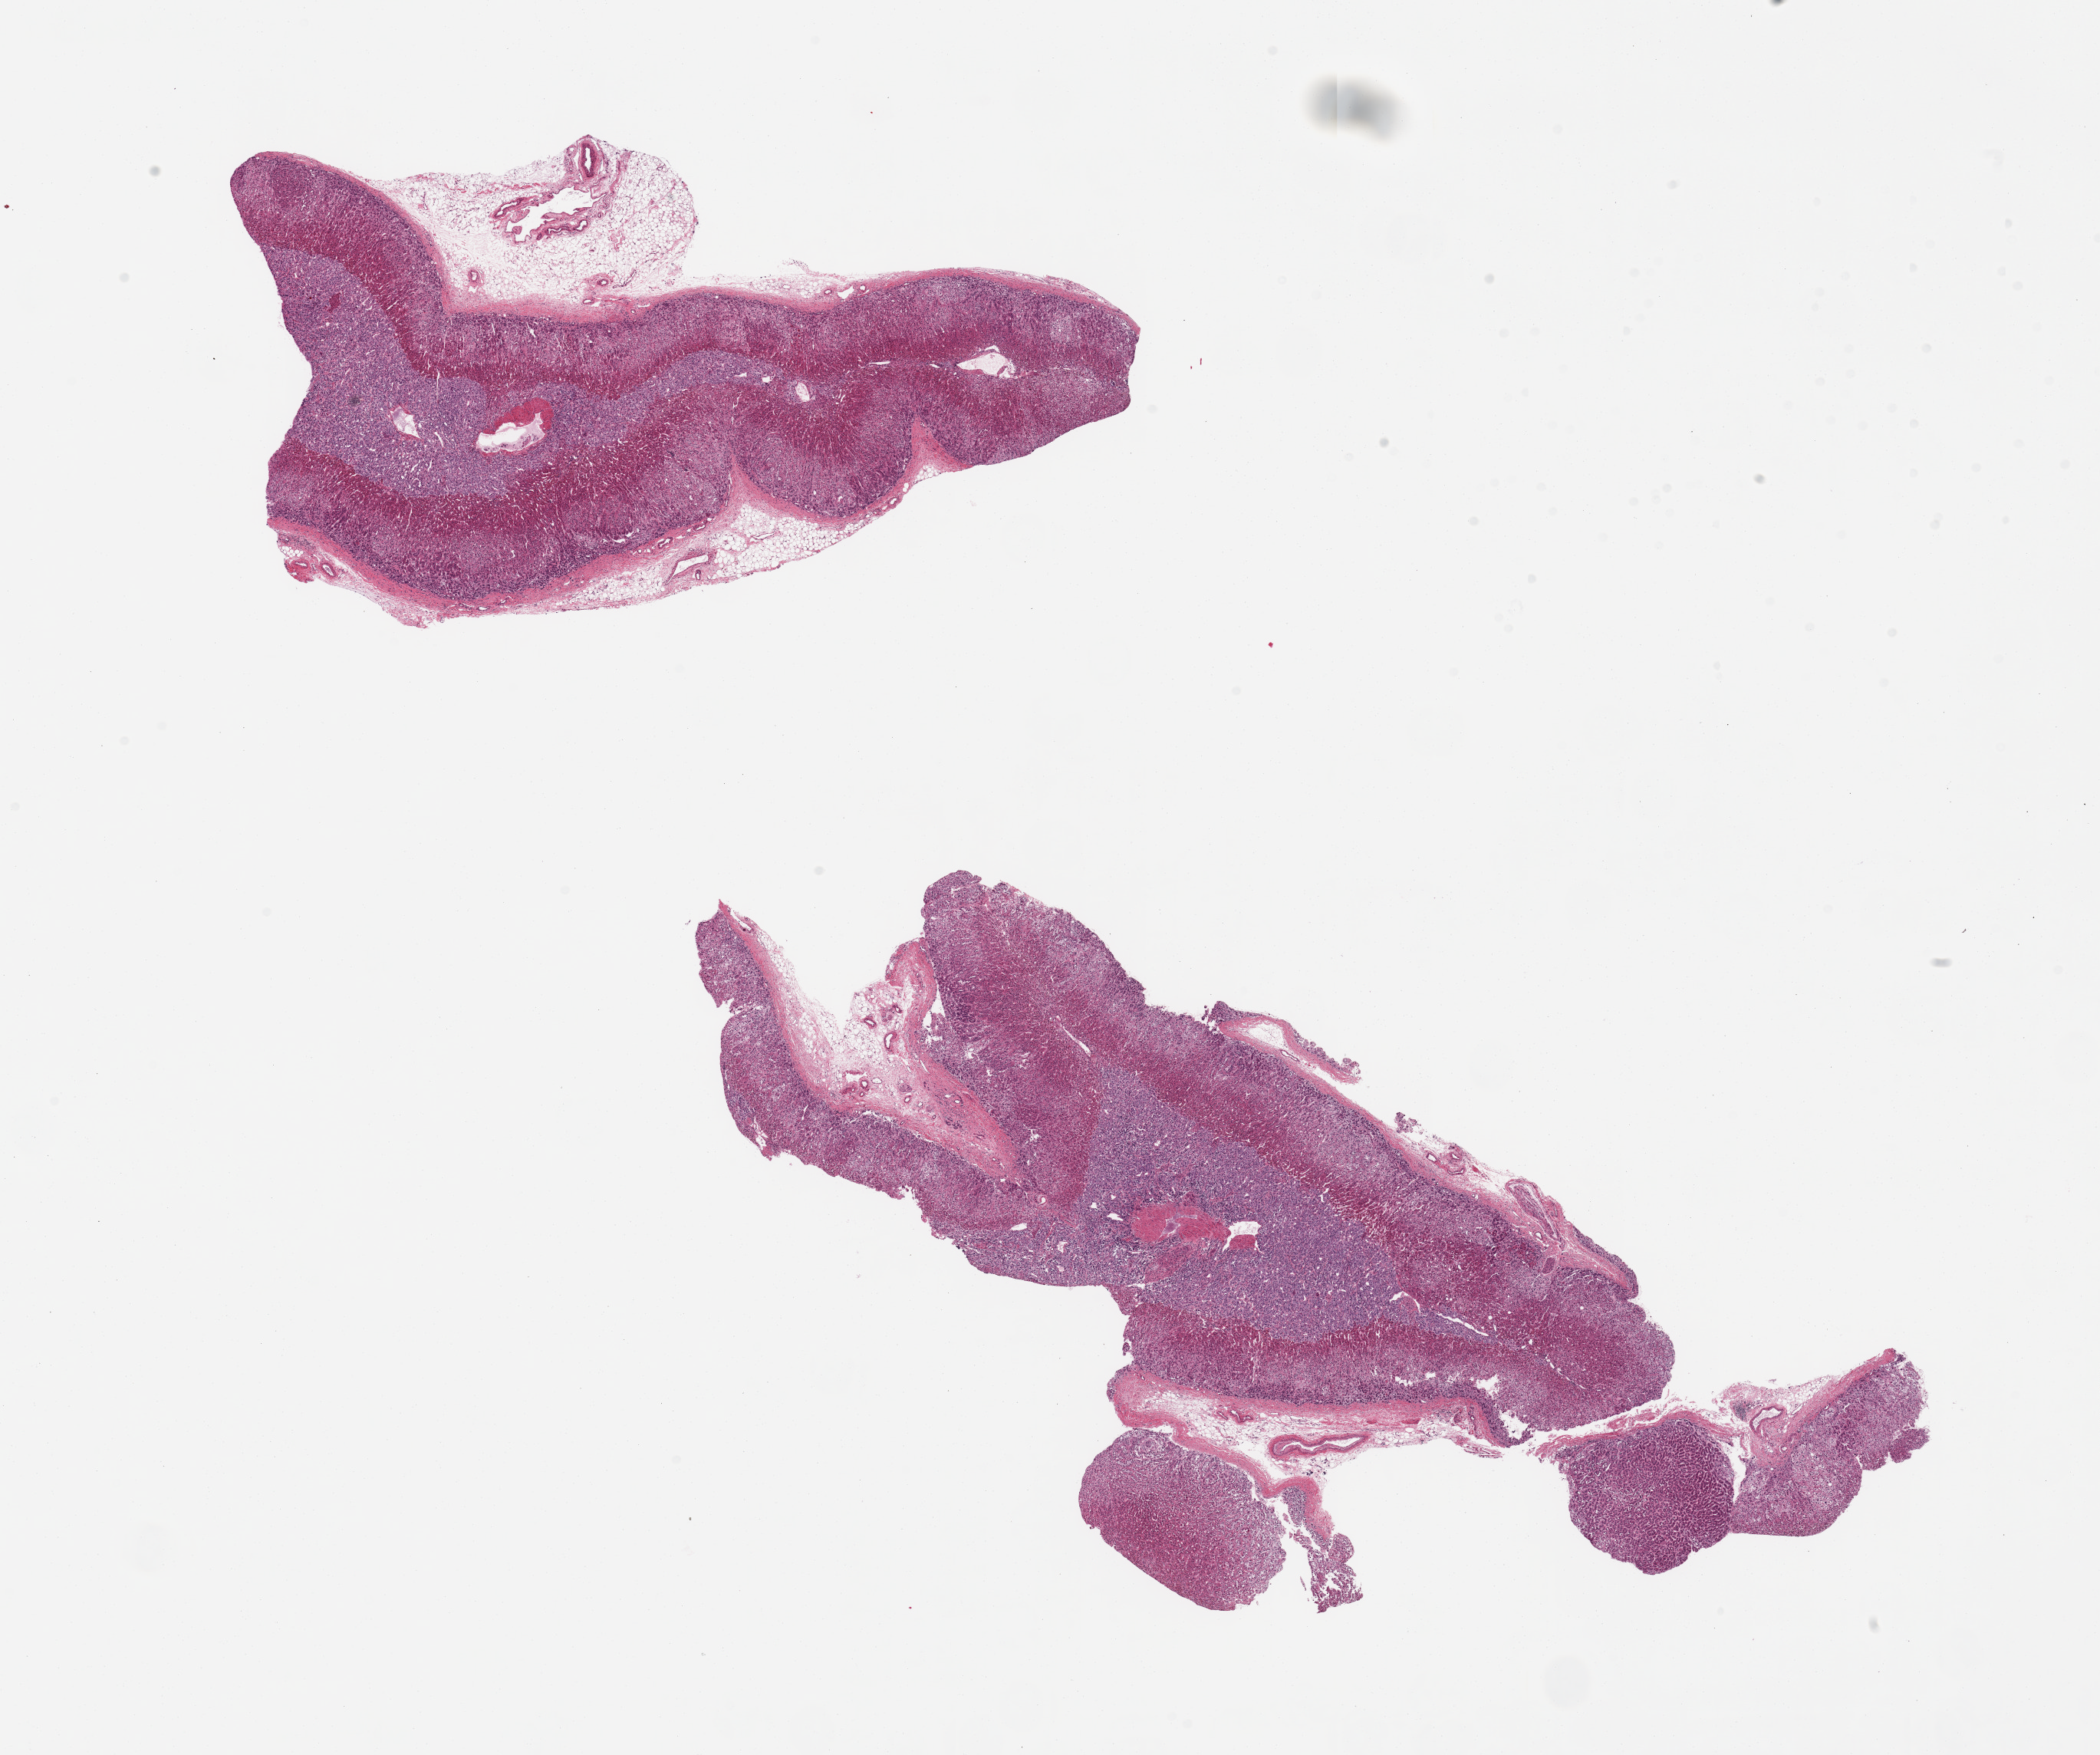
Whole-slide image, hematoxylin and eosin (H&E) stain, brightfield — whole scanned area (about 21.7 x 18.1 mm, from a 20x scan) shown as a low-resolution overview; PAXgene-fixed, paraffin-embedded tissue; sampled site (target tissue): adrenal gland; tissue donor sample. Donor: female.
* pathologist's review note for this sample: 2 pieces; prominent medullary component; 10% external fat